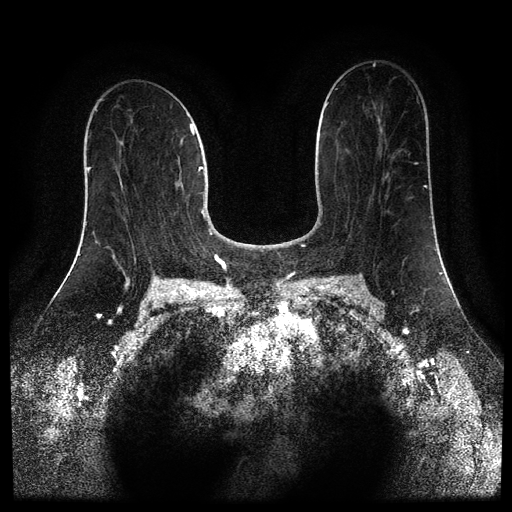
Breast MRI (dynamic contrast-enhanced, multi-phase), one axial slice. Slice 46 of 110 in the series (ordered by position). Dynamic contrast-enhanced series, time point 2 of 5 at this slice position (early post-contrast). 1.5 T. TE 2.6 ms, TR 5.4 ms. 512 × 512 image matrix, field of view 340 × 340 mm. Patient: female, 43 years.
Annotated regions visible in this slice (semi-automatic segmentation, software-assisted and operator-edited):
- breast lesion (labelled 'tumour' in the annotation; benign lesions carry a separate 'benign' label): box from (x=174, y=180) to (x=183, y=189) px